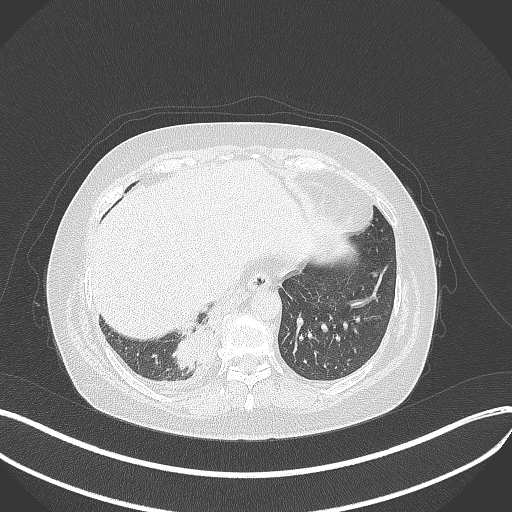
Chest CT, one axial slice. Position 88 of 381 along the scan axis. 120 kVp. Lung window (W 1500 / L -600 HU). 1 mm slice thickness. 512 × 512 image matrix, field of view 400 × 400 mm. Patient: female, 56 years. From the clinical record (not read from this slice): clinical TNM (as recorded): T2b N1 M0.
Annotated regions visible in this slice (rectangle marked by the reading radiologist):
- lung tumour (recorded histology: small cell carcinoma): bounding box (x1, y1, x2, y2) in pixels: (174, 325, 214, 371)